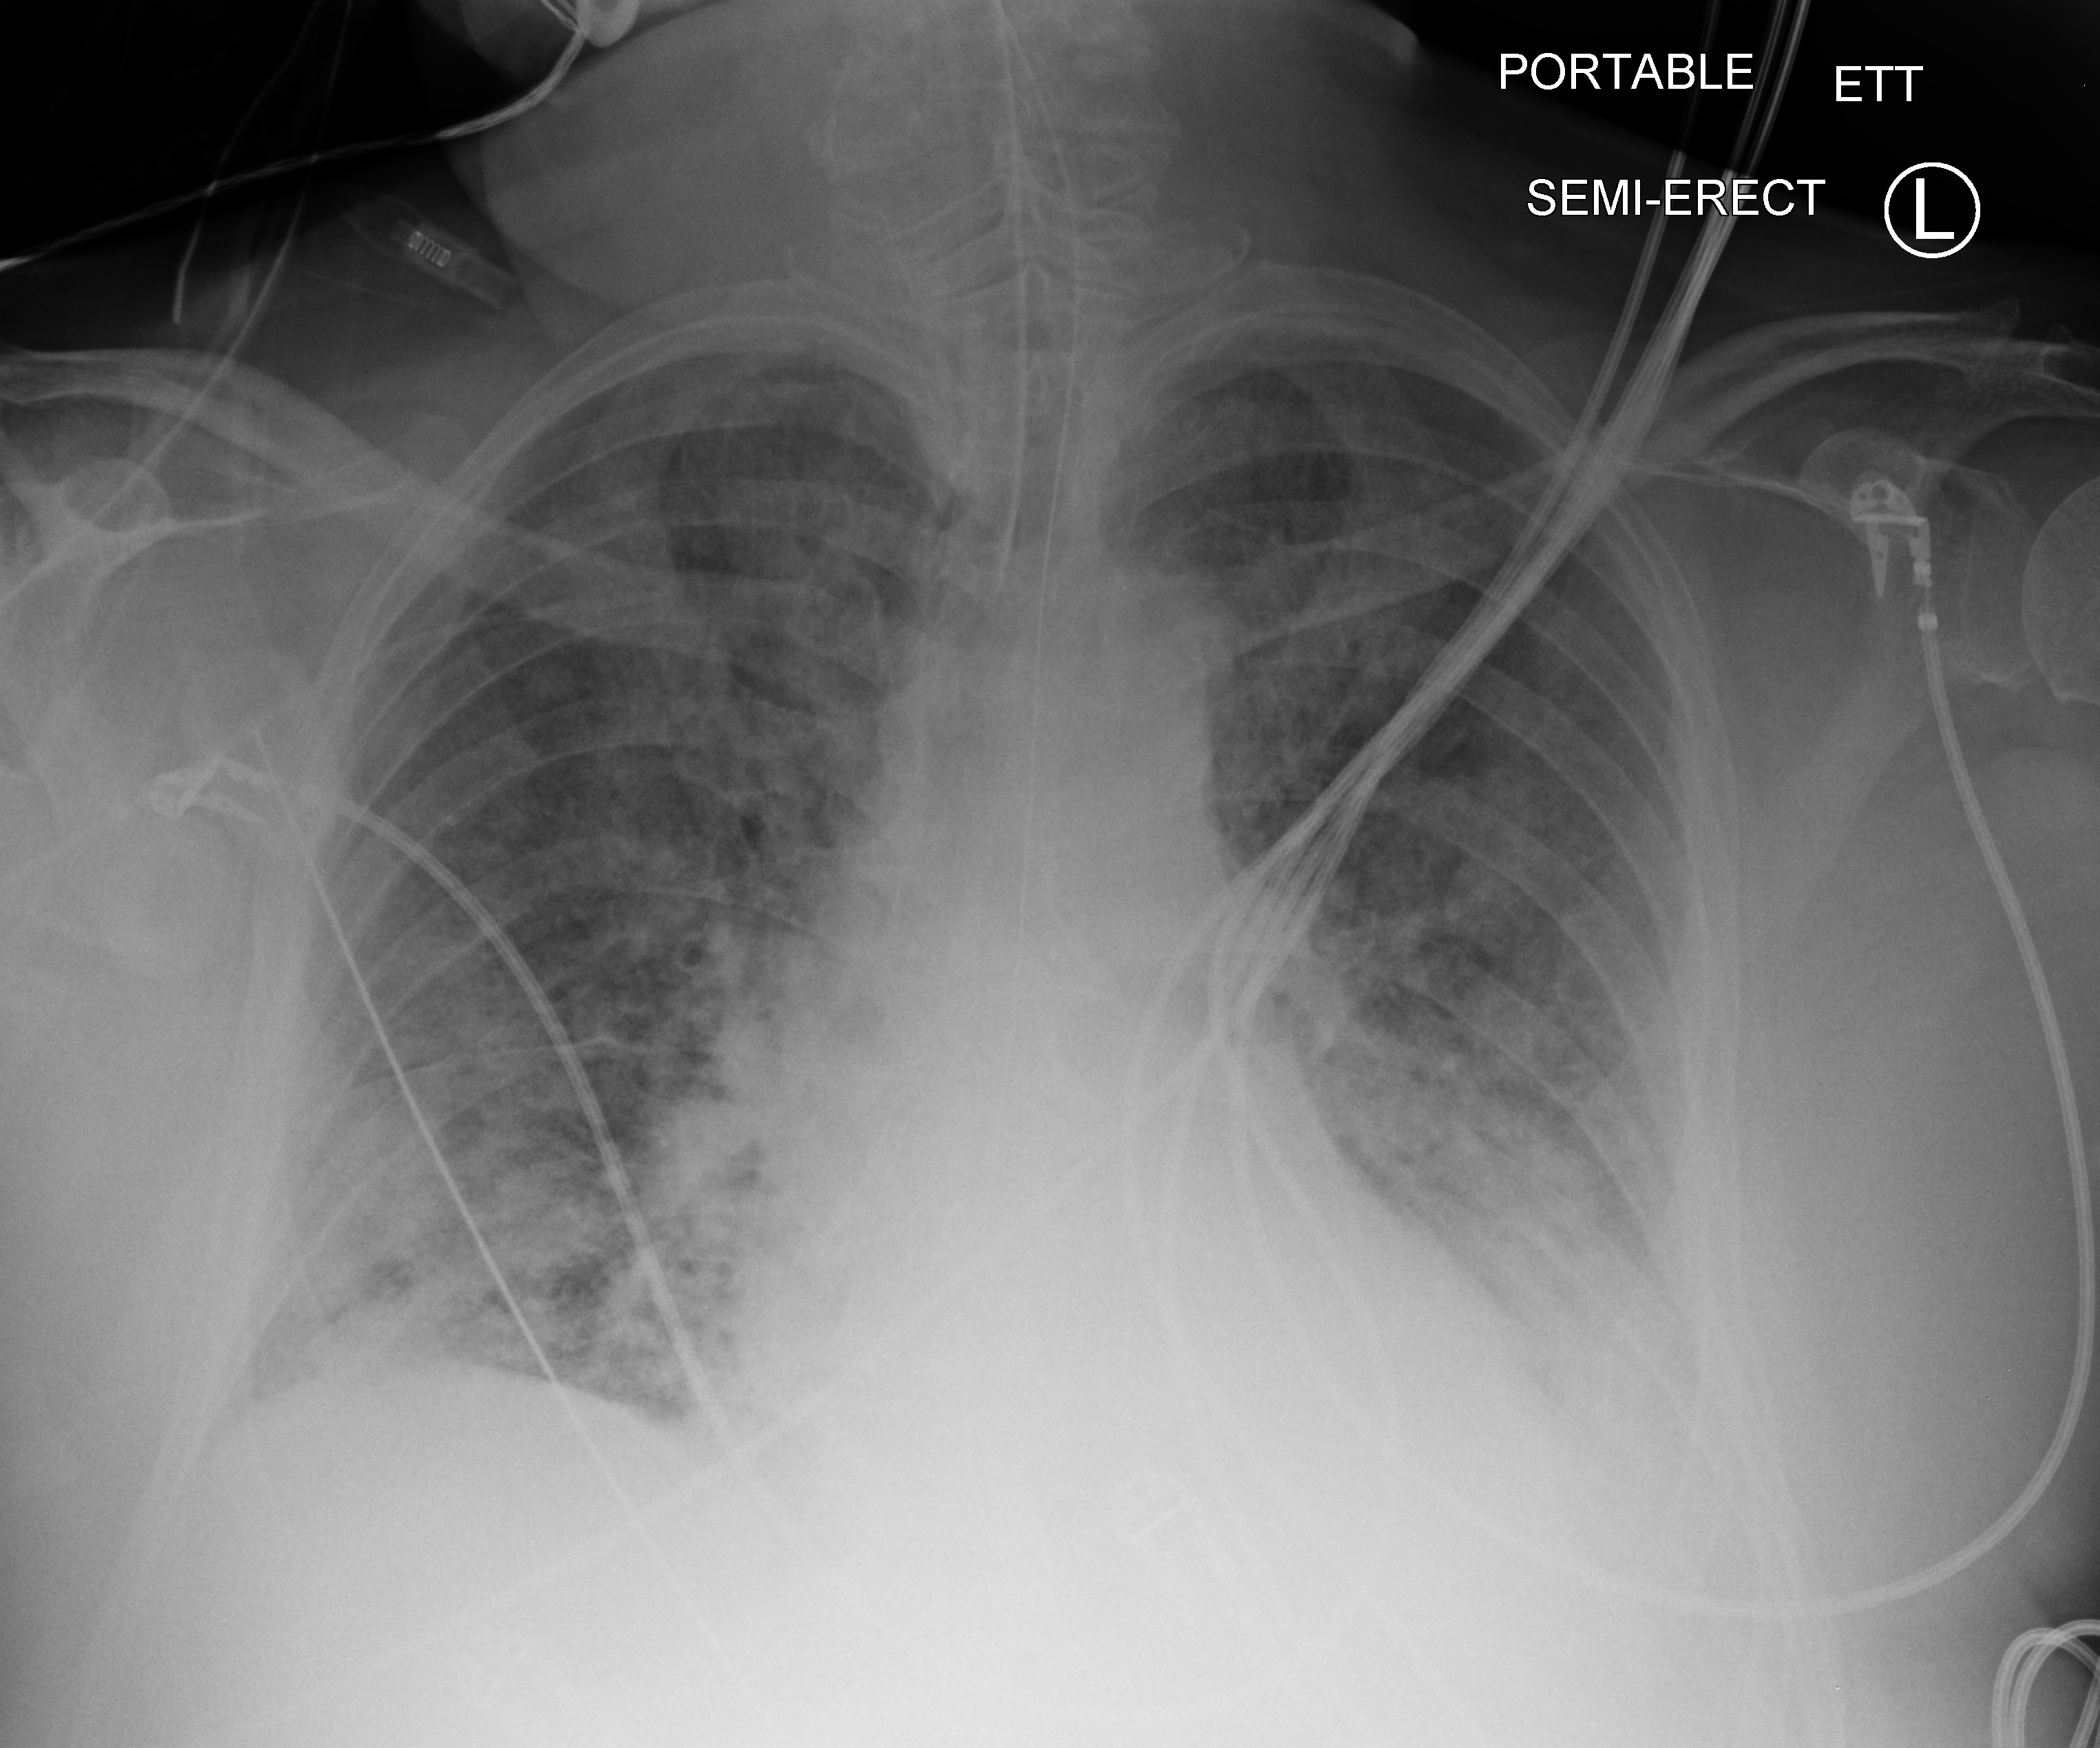
Portable chest radiograph; anteroposterior (AP) projection. Male patient hospitalised with COVID-19, age 60–74 years.
From the hospital-stay record, not from the radiograph (when in the stay this image was taken is not recorded):
- chronic kidney disease (admission record): no
- admitted to intensive care during this hospital stay: yes
- other chronic lung disease (admission record): no